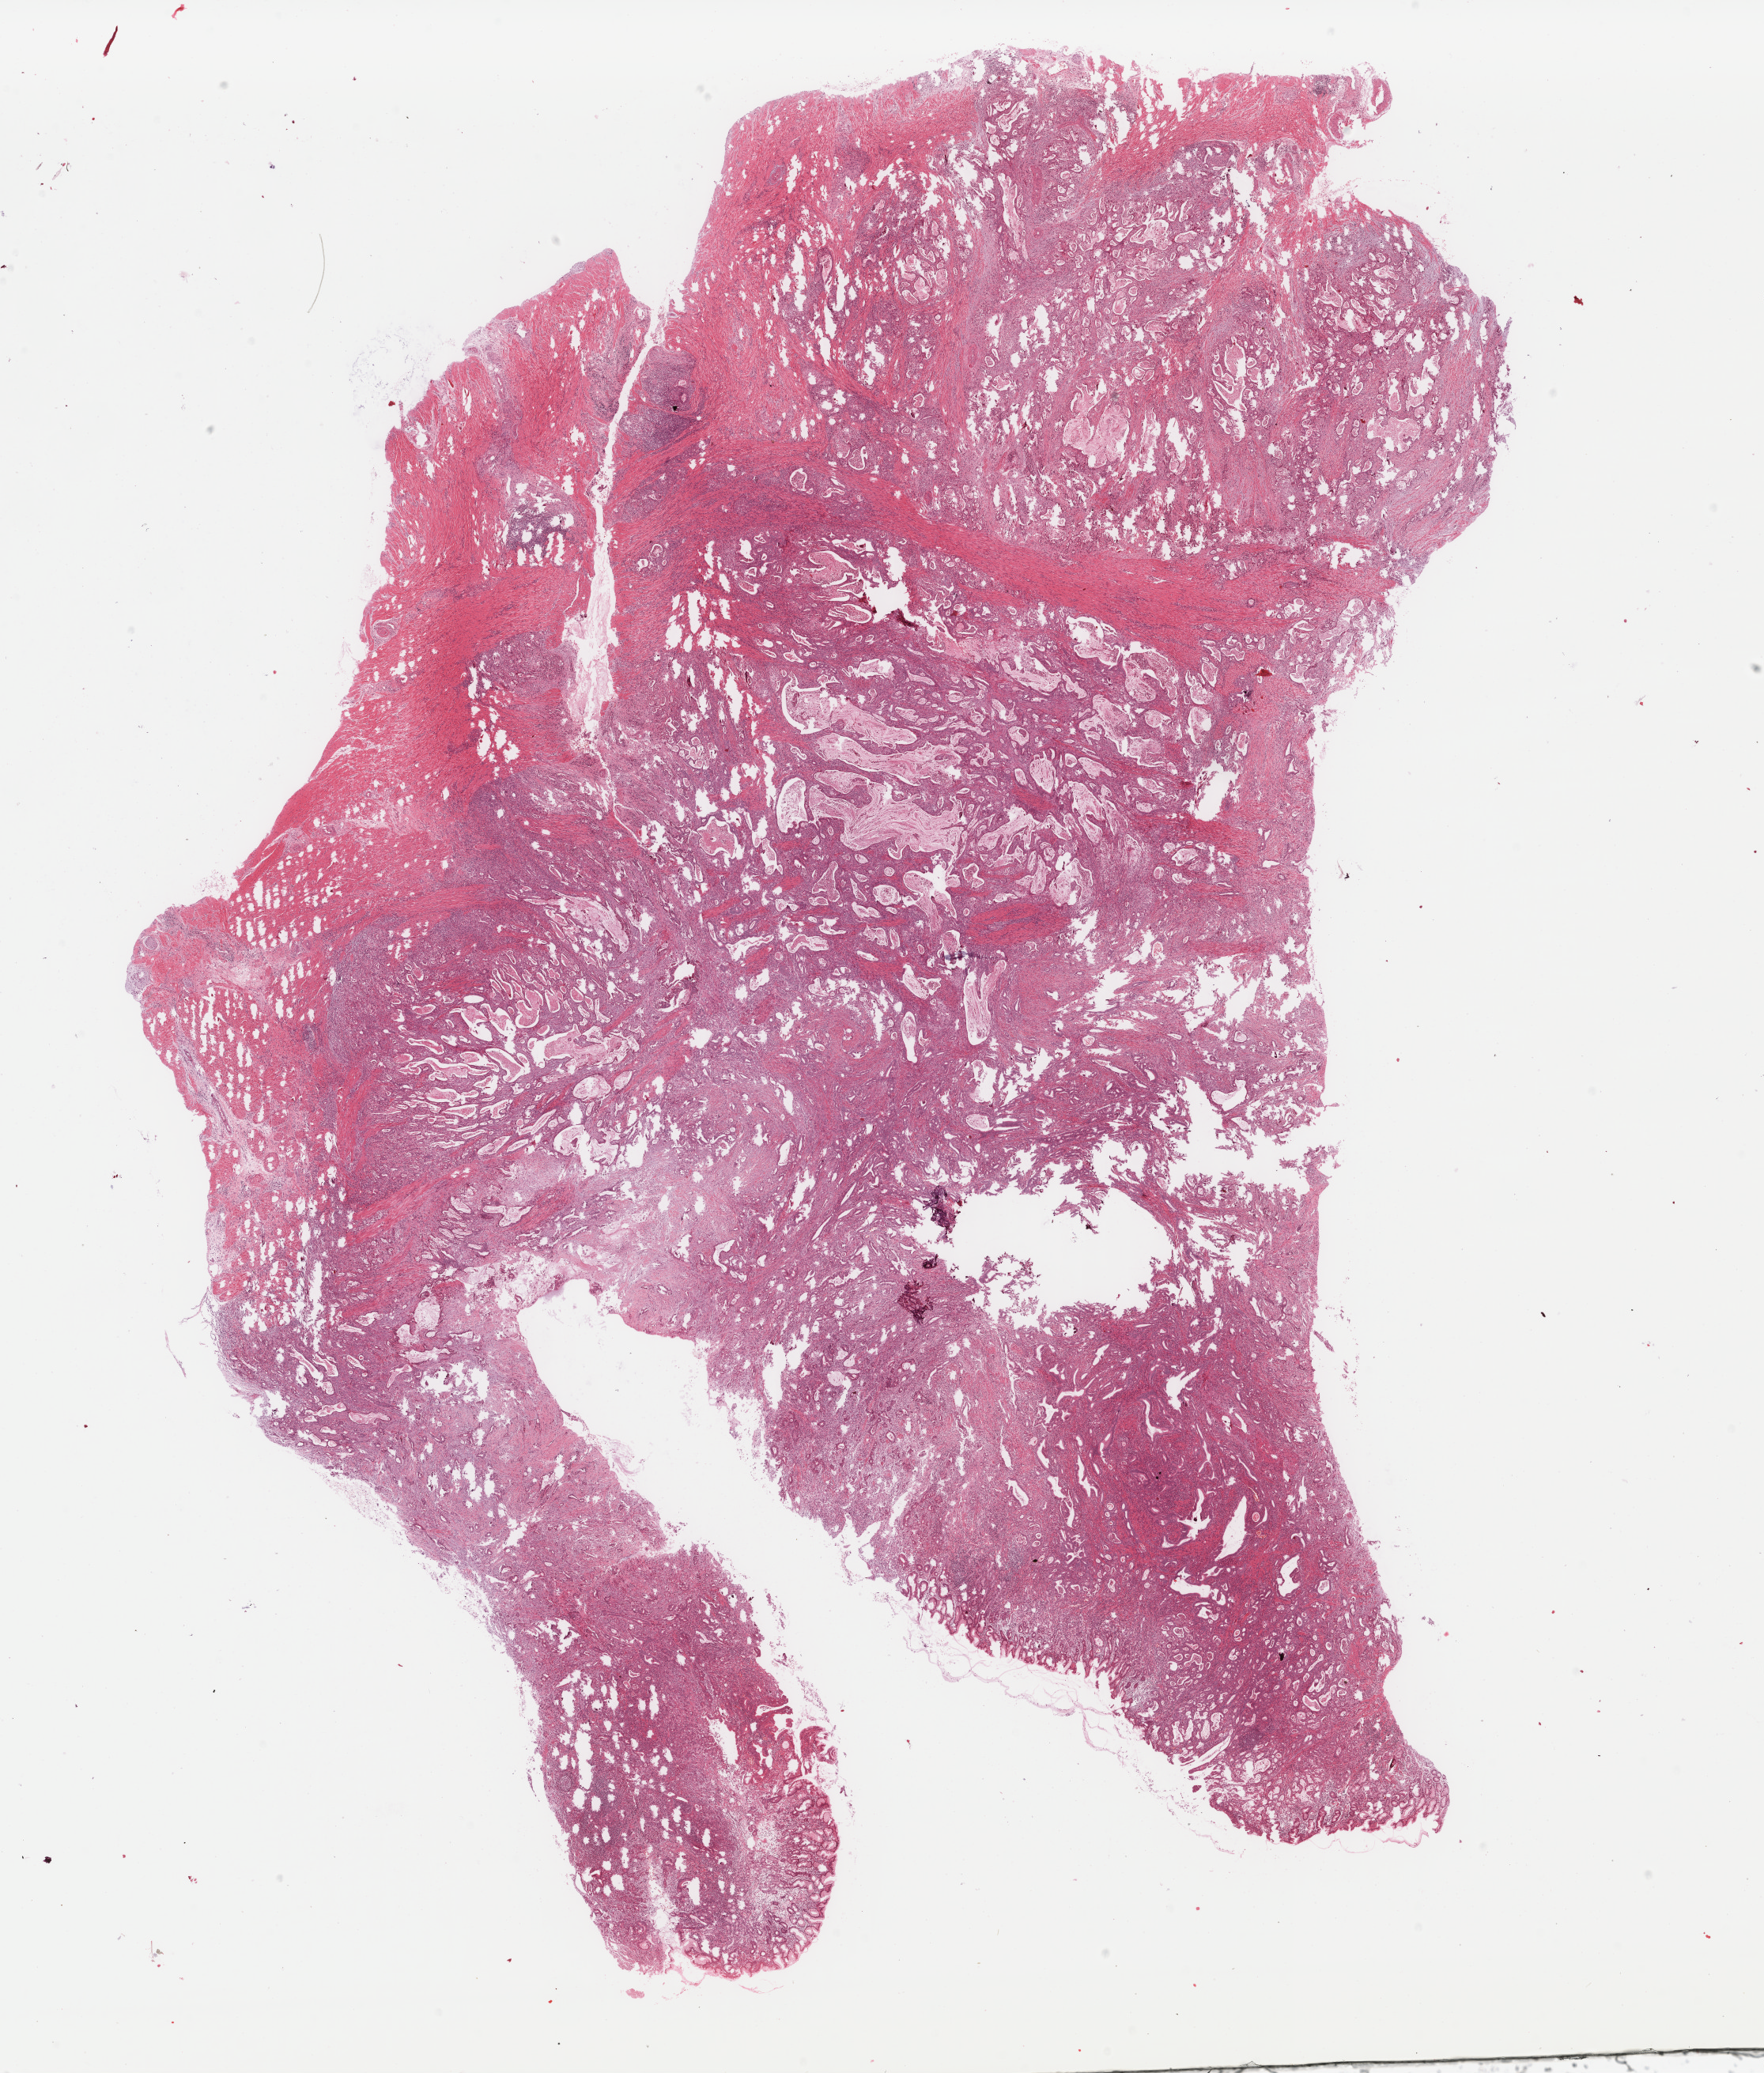
Whole-slide histology image, H&E-stained, whole scanned area (about 17.7 x 20.8 mm) shown as a low-resolution overview; formalin-fixed paraffin-embedded (FFPE) diagnostic section; stomach, primary tumour sample. Male, age 62 years at initial diagnosis.
Pathologic diagnosis: Adenocarcinoma, NOS (gastric antrum).